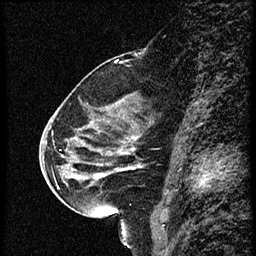
Breast MRI (dynamic contrast-enhanced), one sagittal slice. Position 31 of 56 along the scan axis. Dynamic contrast-enhanced study with each time point stored as its own series, time point 2 of 4 at this slice position (early post-contrast, ordered by acquisition time). 1.5 T. TE 4.2 ms, TR 18.9 ms. 2 mm slice thickness. 256 × 256 image matrix, field of view 200 × 200 mm. Female patient. Case-level facts recorded for this patient, not image findings: setting: breast cancer imaged before/during neoadjuvant chemotherapy; receptor status: HER2-positive.
Annotated regions visible in this slice (semi-automatic segmentation, software-assisted and operator-edited):
- analysis volume of interest (the breast-tissue region the enhancement analysis was run in; not a lesion): box from (x=63, y=80) to (x=161, y=215) px
- tumour enhancement mask (voxels above the 100 % enhancement threshold inside the analysis volume of interest): (x=98, y=138)–(x=136, y=179)